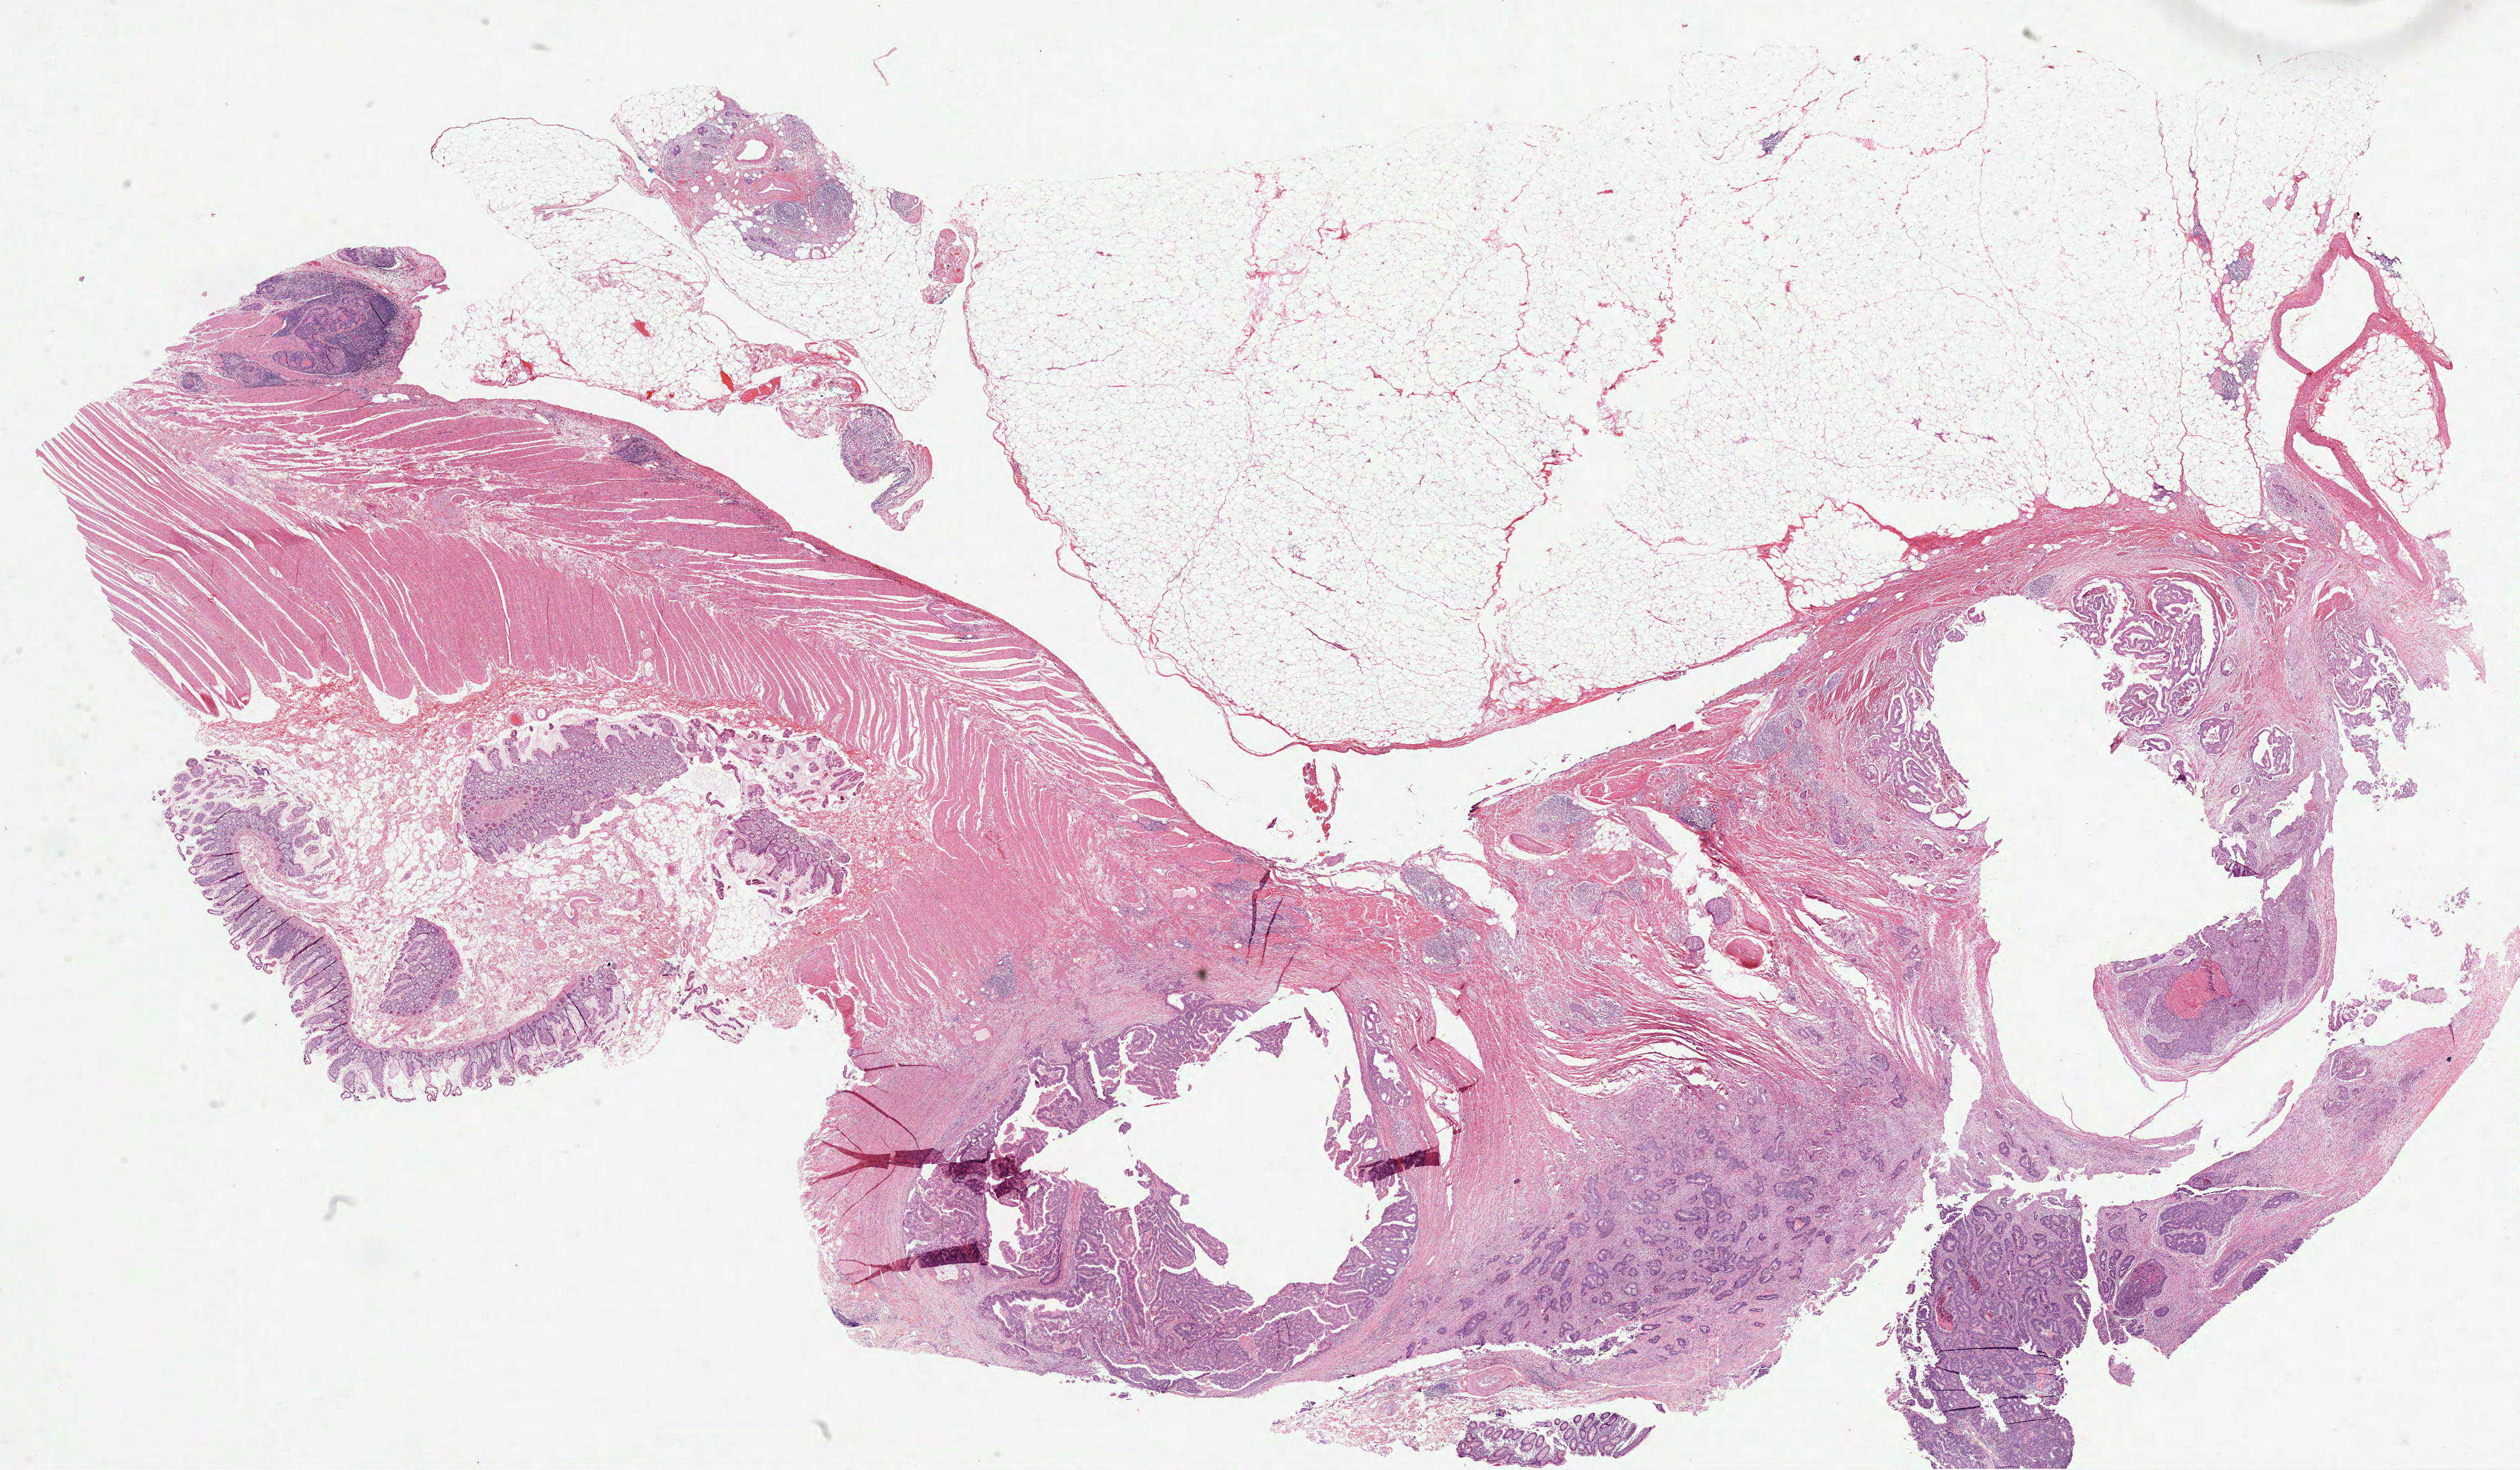
Digitized Hematoxylin and eosin (H&E) stained tissue section (whole slide), low-resolution overview of the scanned area, about 32.4 x 18.9 mm (slide scanned at 40x). Formalin-fixed paraffin-embedded (FFPE) diagnostic section. Colon, primary tumour sample. Female, age 76 years at initial diagnosis.
Lymph nodes positive (case pathology): 50 of 59 examined. Histologic diagnosis: Adenocarcinoma, NOS (cecum). AJCC pathologic stage: IV (6th edition). TNM: T3 N2 M1.